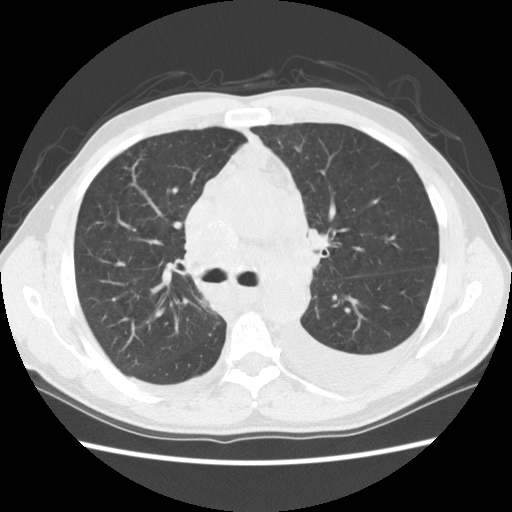
Axial slice from a low-dose chest CT screening exam, first (baseline) screen, lung window (W 1500 / L -600 HU), standard (soft-tissue) reconstruction kernel (STANDARD), 140 kVp, slice 41 of 135 in the series, 512 × 512 image matrix, field of view 346 × 346 mm. Male participant, aged 60 years at enrolment.
• Lesion marked by an expert reader, bounding box [x1, y1, x2, y2] px = [178, 235, 291, 325].
• Screening reader's record for this exam: no non-calcified nodule ≥4 mm recorded.
• Official screen result: negative screen, significant abnormalities not suspicious for lung cancer.
• Lung cancer was diagnosed 12 days after this screen: squamous cell carcinoma, NOS, carina, poorly differentiated (G3), stage IV (AJCC 6th edition).